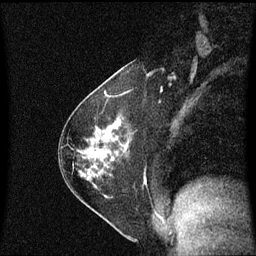
Breast MRI (dynamic contrast-enhanced), one sagittal slice. Position 34 of 60 along the scan axis. Dynamic contrast-enhanced series, image 2 of 3 at this slice position (ordered by acquisition). 1.5 T. TE 4.2 ms, TR 8.4 ms. 256 × 256 image matrix. Female patient, age 54 years. From the clinical record (not read from this slice): setting: breast cancer imaged before/during neoadjuvant chemotherapy; receptor status: HER2-positive.
Outlined on this slice (semi-automatic segmentation, software-assisted and operator-edited):
- analysis volume of interest (the breast-tissue region the enhancement analysis was run in; not a lesion): bounding box <68,116,132,189> (left, top, right, bottom; pixels)
- tumour enhancement mask (voxels above the 70 % enhancement threshold inside the analysis volume of interest): <117,122,121,126>